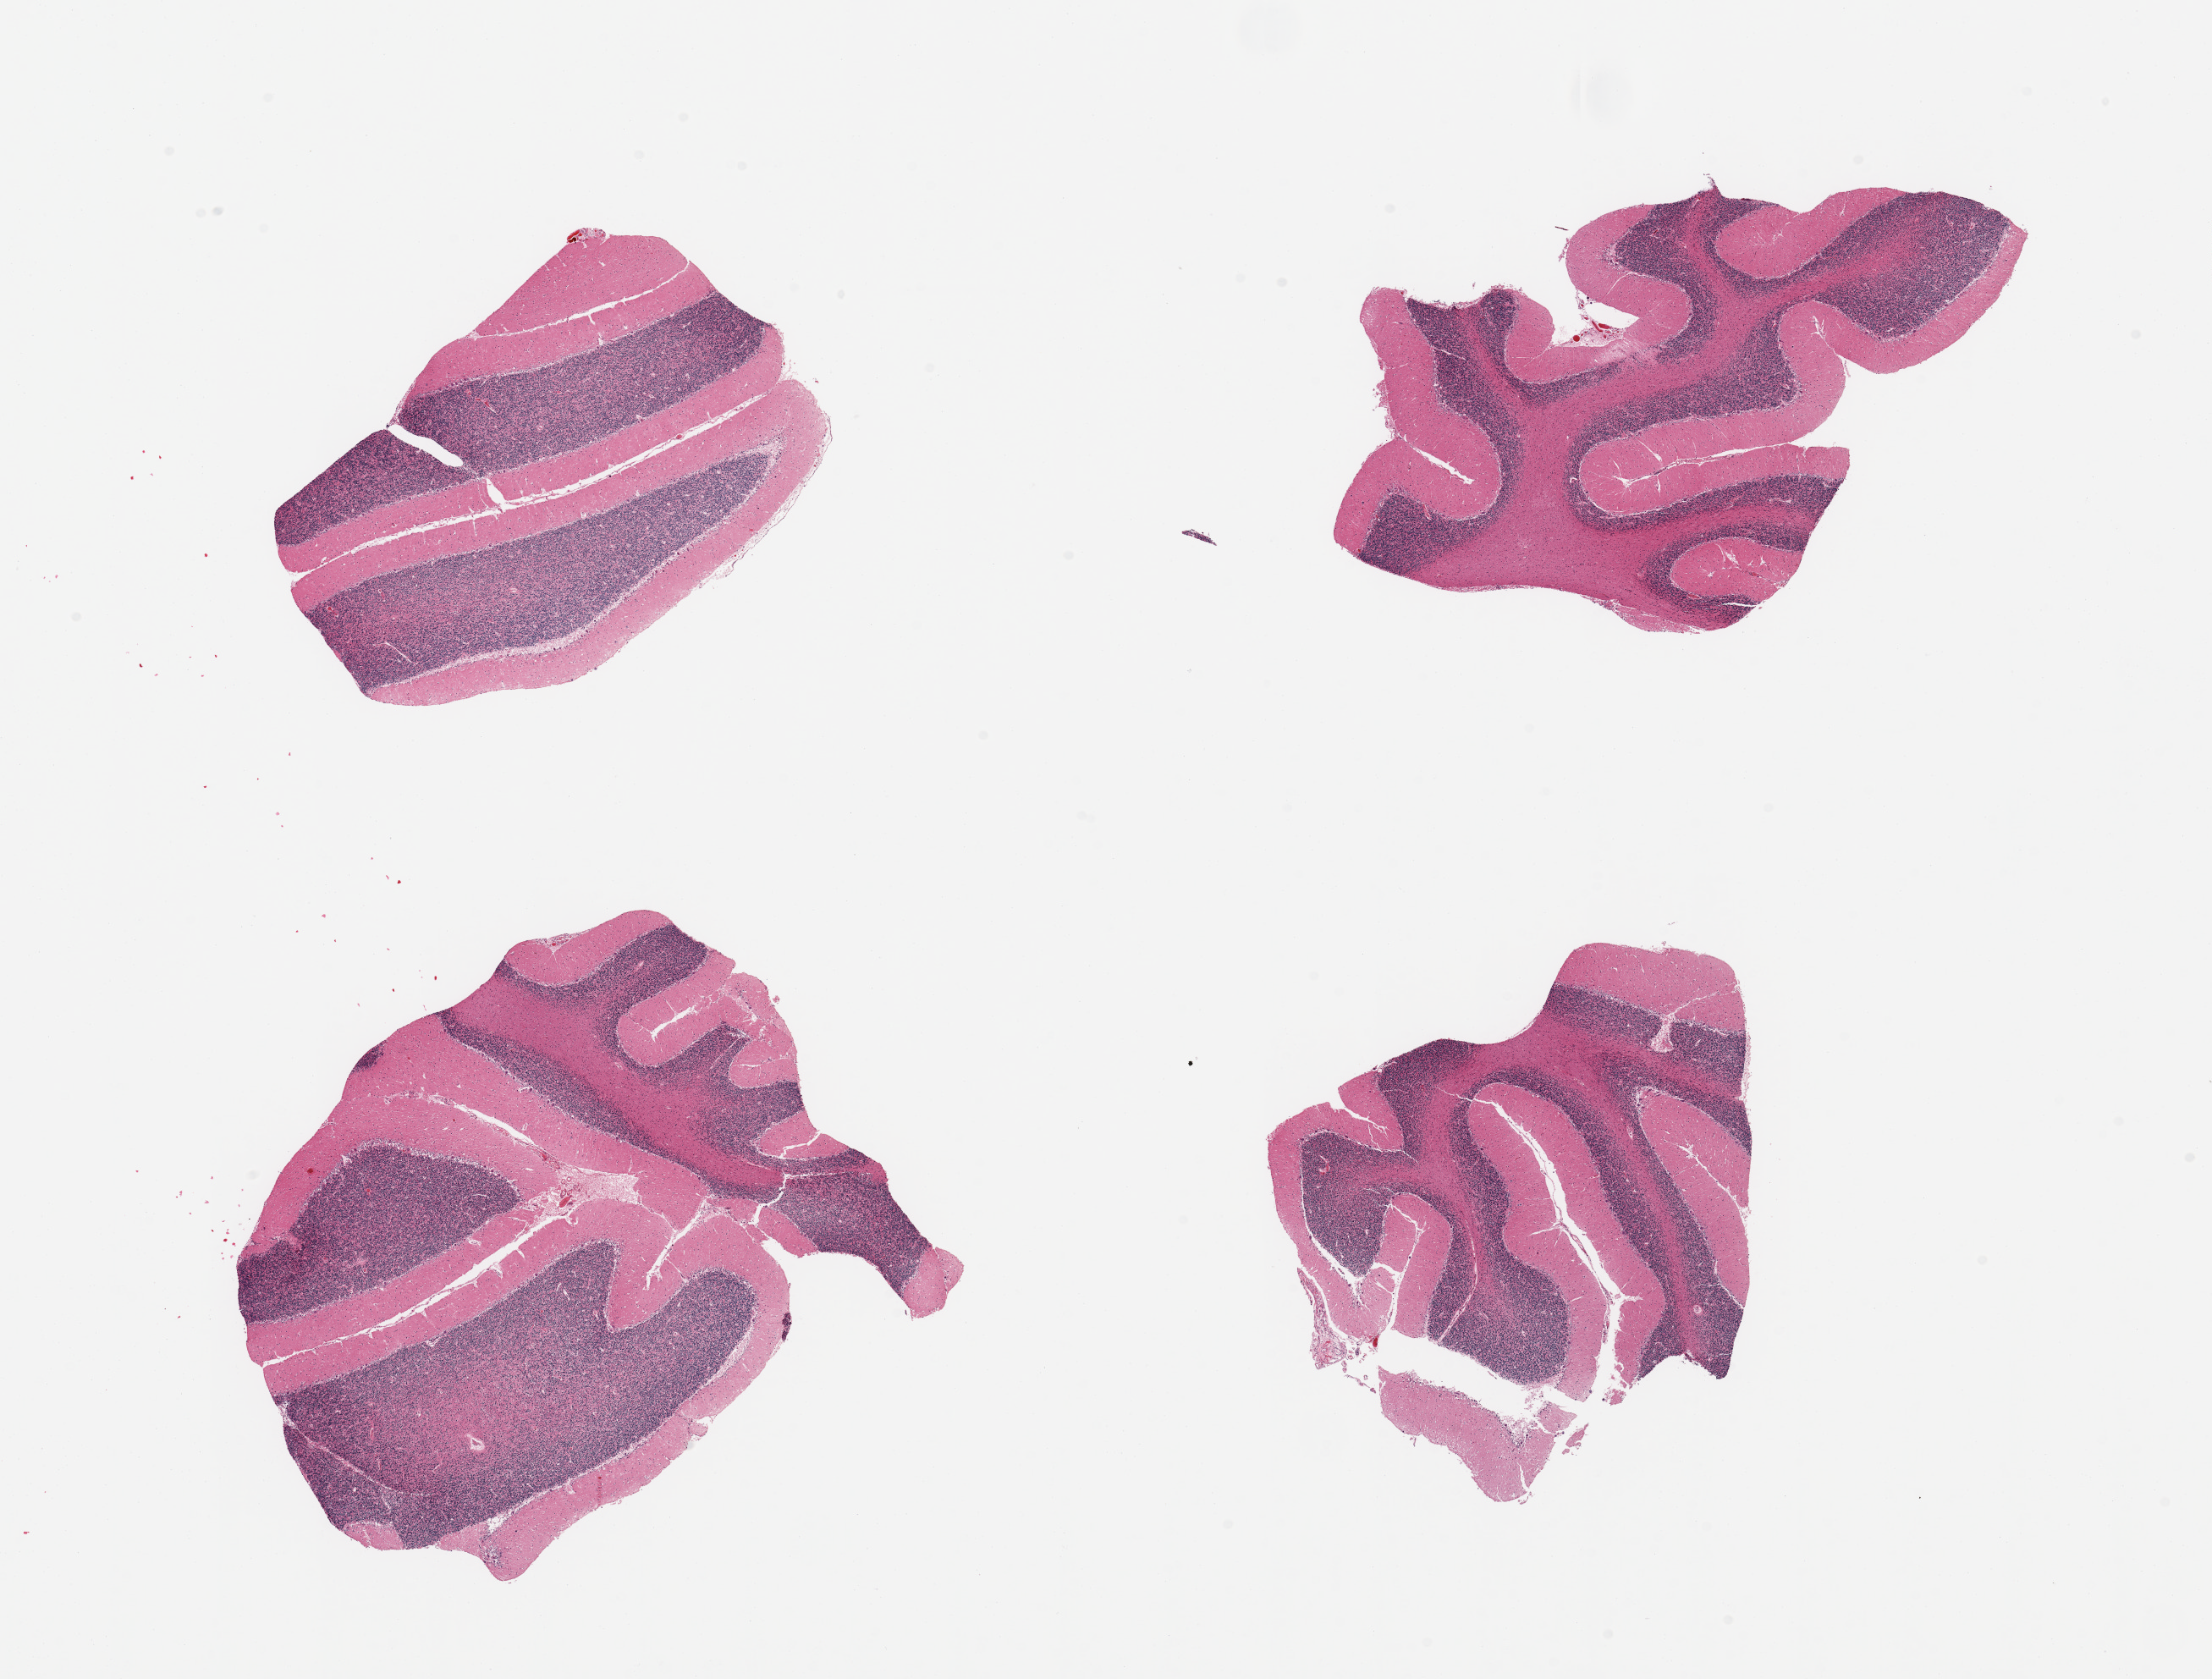
Digitized hematoxylin and eosin (H&E)-stained section, brightfield — whole scanned area (about 20.7 x 15.7 mm, slide scanned at 20x) shown as a low-resolution overview, PAXgene-fixed paraffin-embedded (PFPE) section, sampled site (target tissue): cerebellum, tissue donor sample.
Pathologist's review note for this sample: 2 pieces.